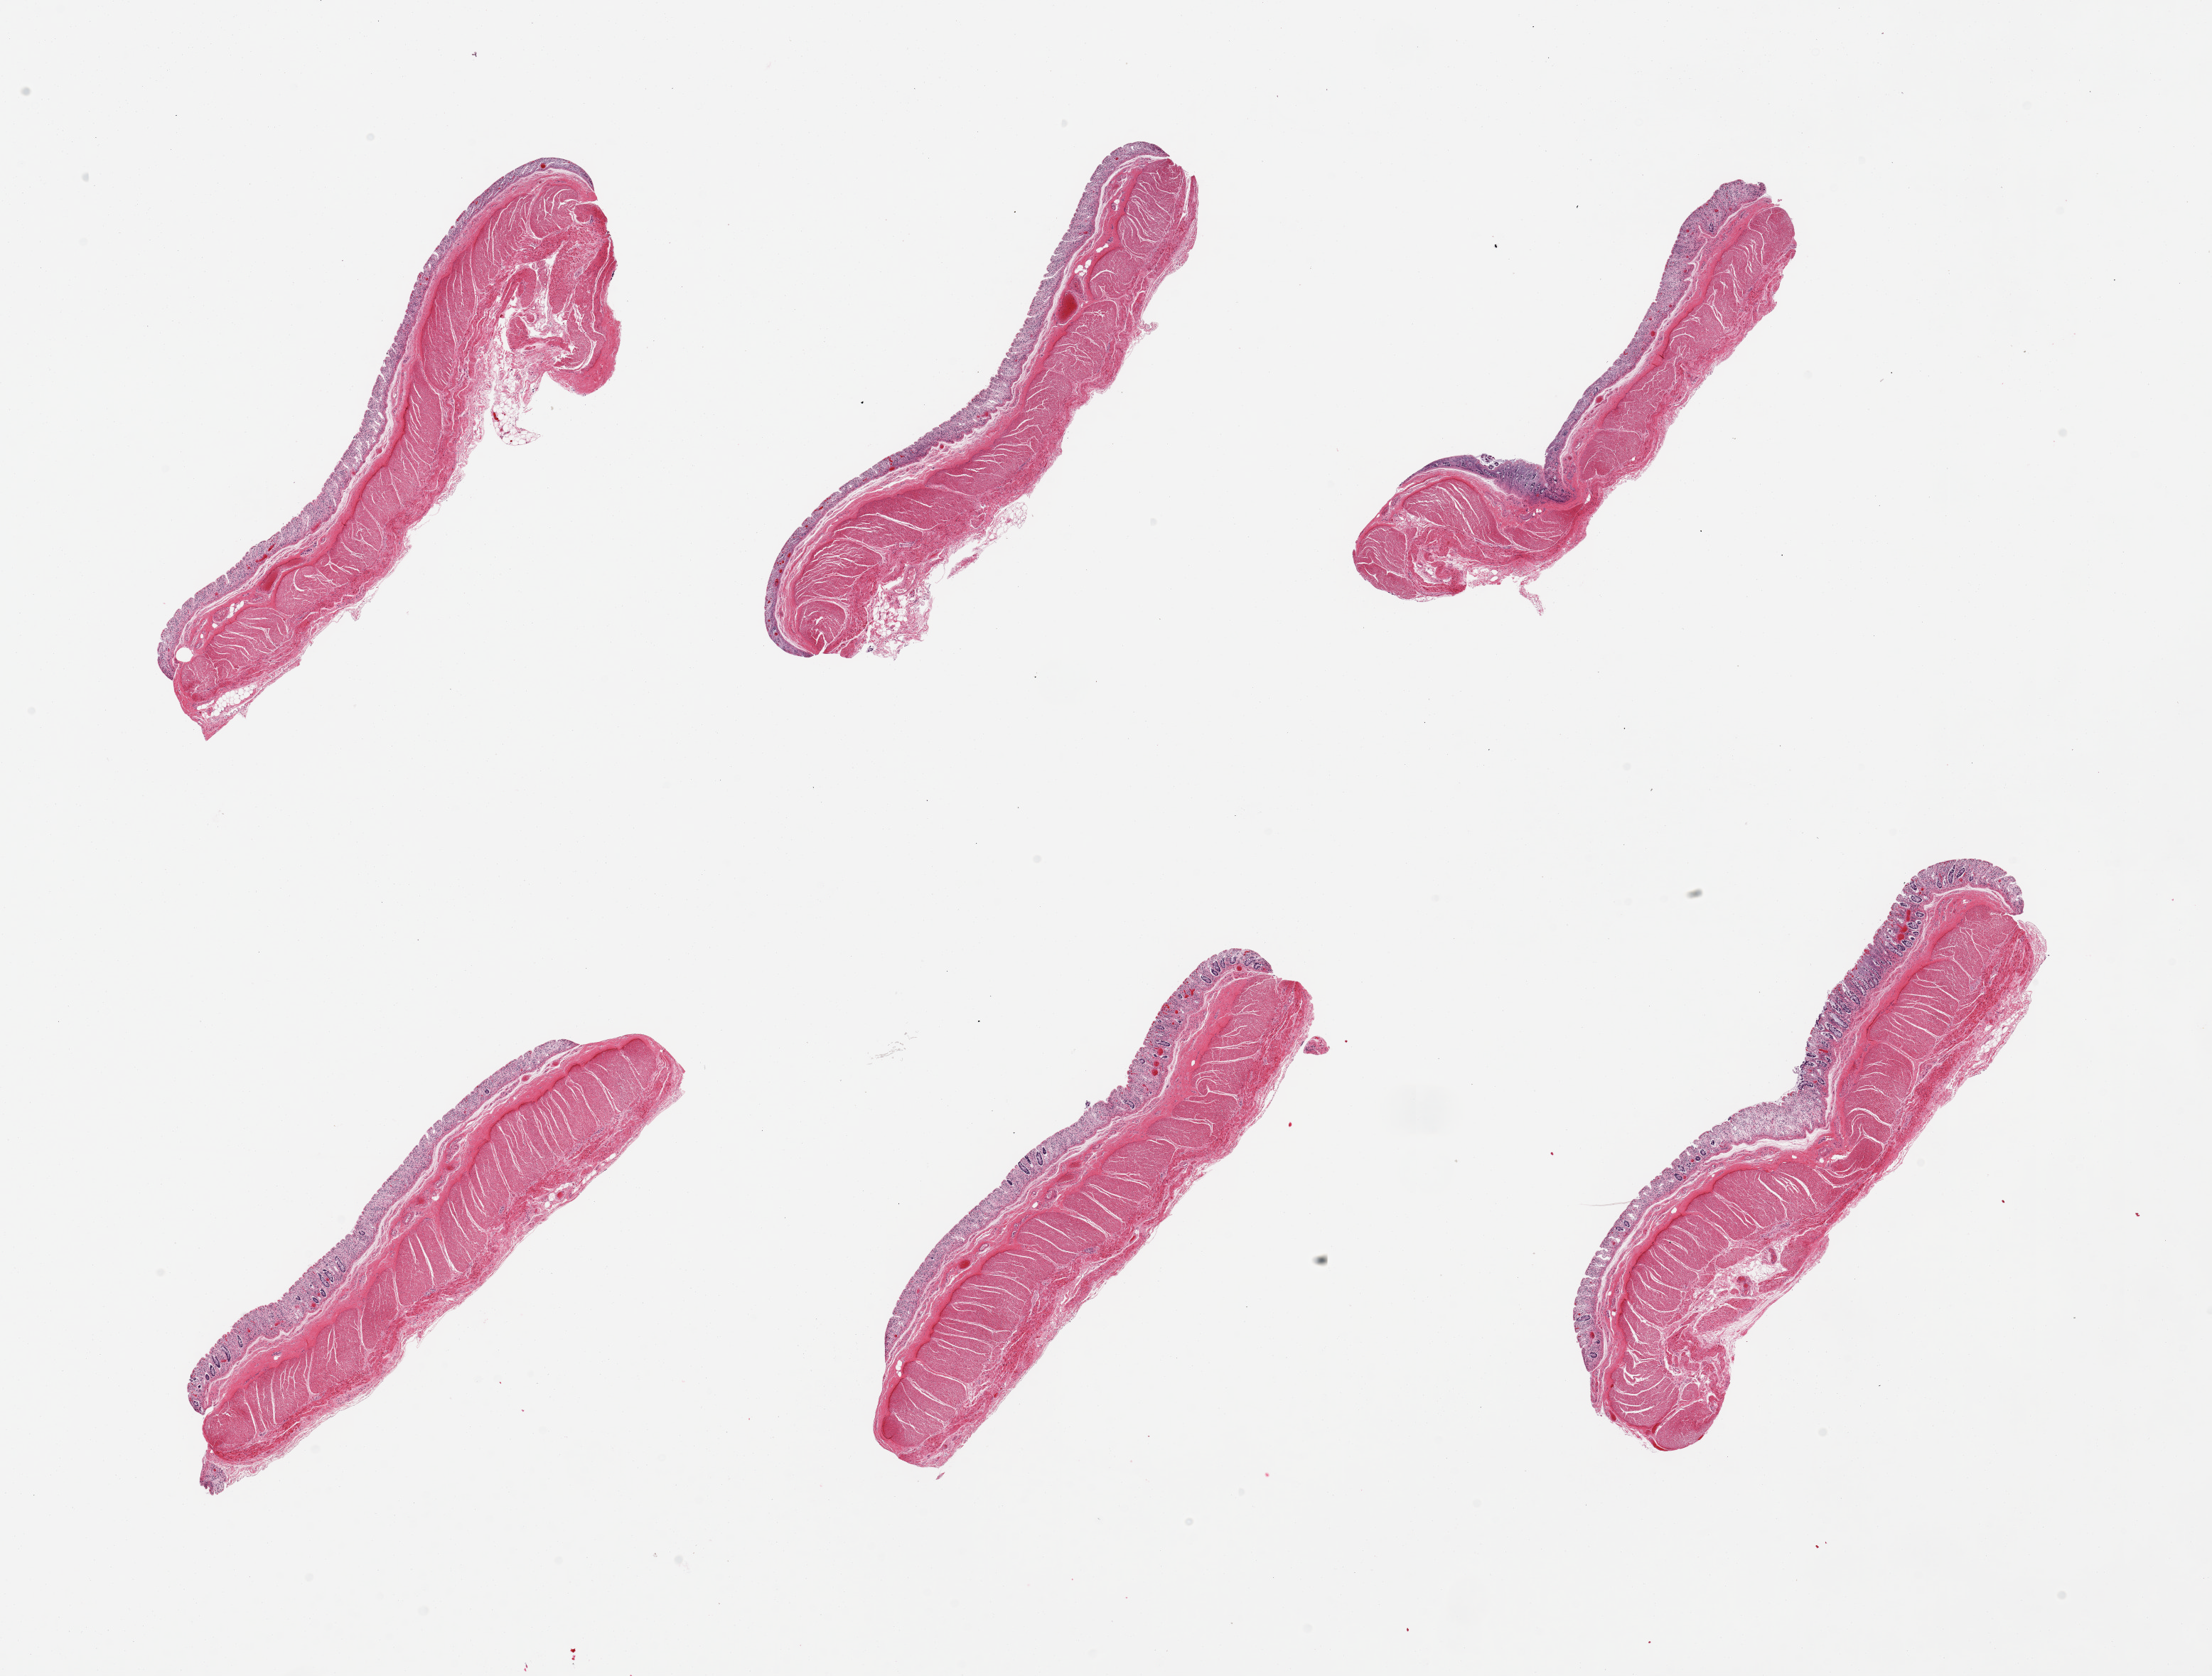
Whole-slide image, H&E stain, shown as a low-resolution overview of the whole scanned area (about 24.6 x 18.6 mm); PAXgene-fixed, paraffin-embedded tissue; sampled site (target tissue): transverse colon; tissue donor sample. Donor sex: male.
Pathologist's review note for this sample: 6 pieces, glandular mucosa badly preserved, ~0.25mm thick.